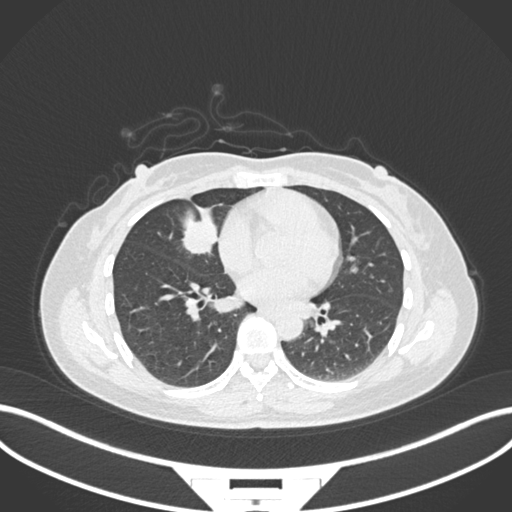
Chest CT, one axial slice; position 73 of 171 along the scan axis; reconstruction kernel B30f; 120 kVp; lung window (W 1500 / L -600 HU); 1 mm slice thickness; 512 × 512 image matrix. Female patient, age 43 years. Case-level facts recorded for this patient, not image findings: clinical TNM (as recorded): T1c N3 M1; histopathological grade: G1.
Outlined on this slice (bounding box drawn by a radiologist):
- lung tumour (recorded histology: adenocarcinoma): bounding box (x1, y1, x2, y2) in pixels: (182, 211, 222, 257)